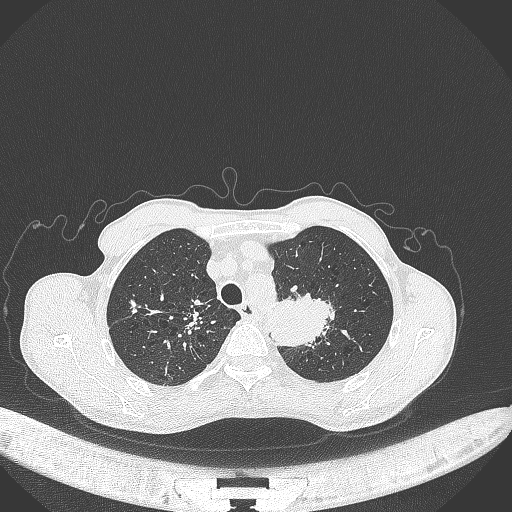
Chest CT, one axial slice. Slice 343 of 386 in the series (ordered by position). Reconstruction kernel B70f. 120 kVp. Lung window (W 1500 / L -600 HU). 512 × 512 image matrix, field of view 400 × 400 mm. Male patient, age 65 years. Case-level facts recorded for this patient, not image findings: clinical TNM (as recorded): T2b N0 M0.
Structures marked on this image (bounding box drawn by a radiologist):
- lung tumour (recorded histology: adenocarcinoma): box from (x=269, y=288) to (x=335, y=349) px